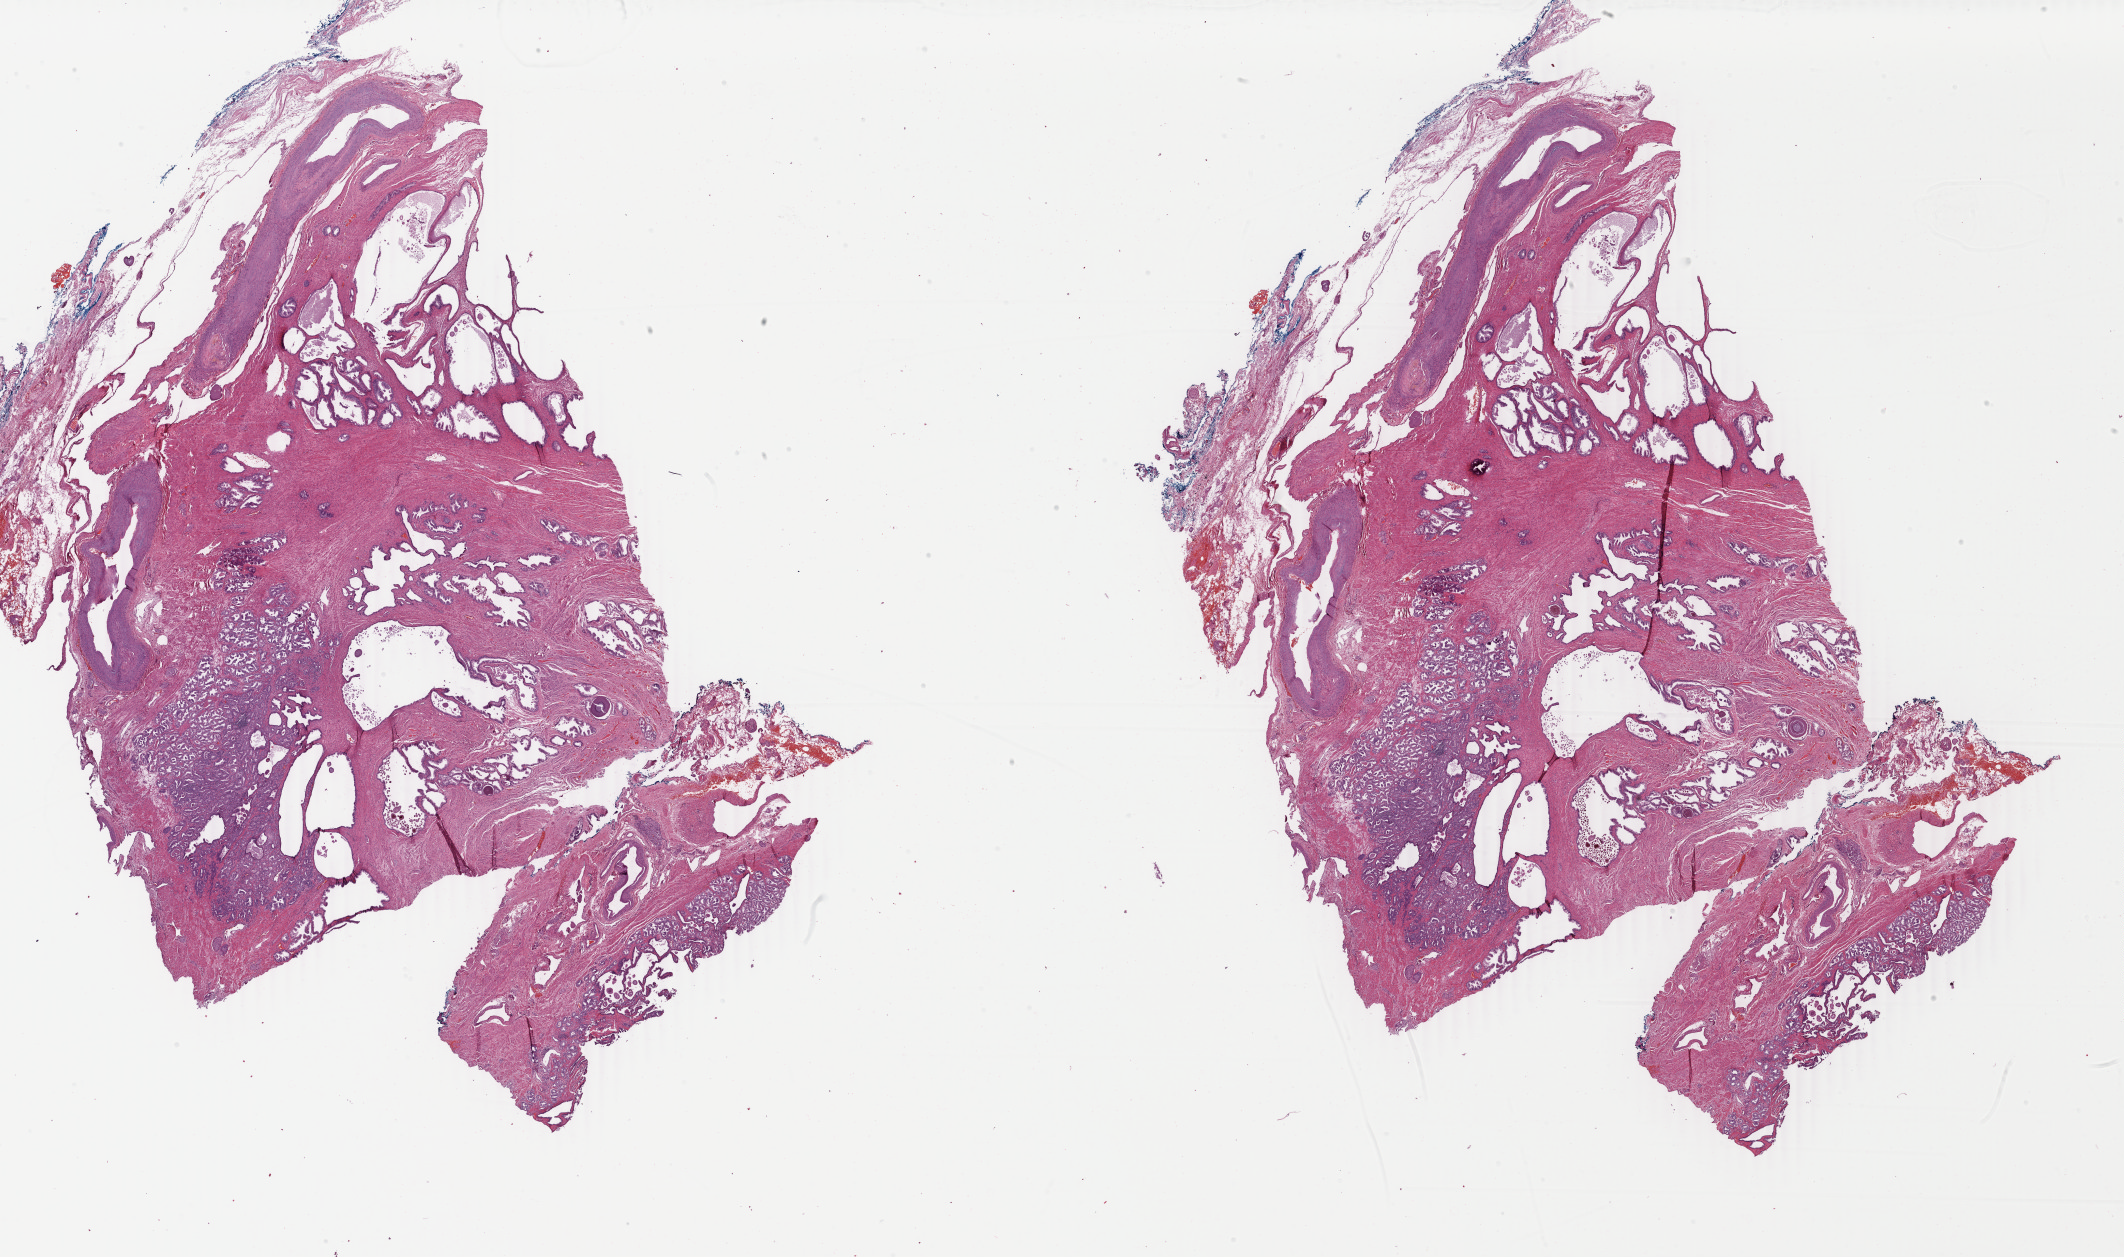
Digitized H&E tissue section (whole slide) — a low-resolution overview of the entire scanned area, about 33.8 x 20.0 mm. Formalin-fixed paraffin-embedded (FFPE) diagnostic section. Primary tumour sample from the prostate. Male, age 63 years at initial diagnosis. Gleason score: 7 (3+4).
- pathologic diagnosis: Adenocarcinoma, NOS (prostate gland)
- laterality: bilateral